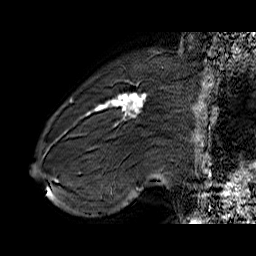
Breast MRI (dynamic contrast-enhanced), one sagittal slice; slice 16 of 60 in the series (ordered by position); dynamic contrast-enhanced series, time point 2 of 6 at this slice position (early post-contrast); 1.5 T; TE 6.4 ms, TR 32.9 ms; 4 mm slice thickness; 256 × 256 image matrix, field of view 200 × 200 mm. Female patient. Case-level facts recorded for this patient, not image findings: setting: breast cancer imaged before/during neoadjuvant chemotherapy; receptor status: HER2-positive.
Structures marked on this image (semi-automatic segmentation, software-assisted and operator-edited):
- analysis volume of interest (the breast-tissue region the enhancement analysis was run in; not a lesion): box from (x=71, y=80) to (x=155, y=146) px
- tumour enhancement mask (voxels above the 100 % enhancement threshold inside the analysis volume of interest): (x=71, y=93)–(x=146, y=119)